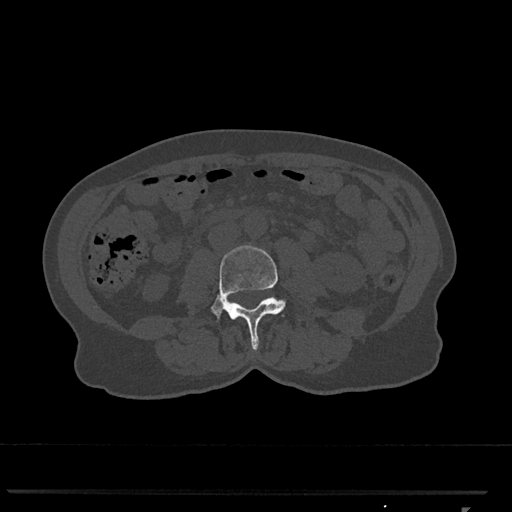
CT including the spine, one axial slice; reconstruction kernel Br40s/3; 120 kVp; bone window (W 1800 / L 400 HU); 0.5 mm slice thickness; 512 × 512 image matrix, field of view 380 × 380 mm. Patient: female, 62 years. Case-level facts recorded for this patient, not image findings: primary cancer: renal.
Structures marked on this image (semi-automatic segmentation, software-assisted and operator-edited):
- L3 vertebra: bounding box <211,245,286,350> (left, top, right, bottom; pixels)